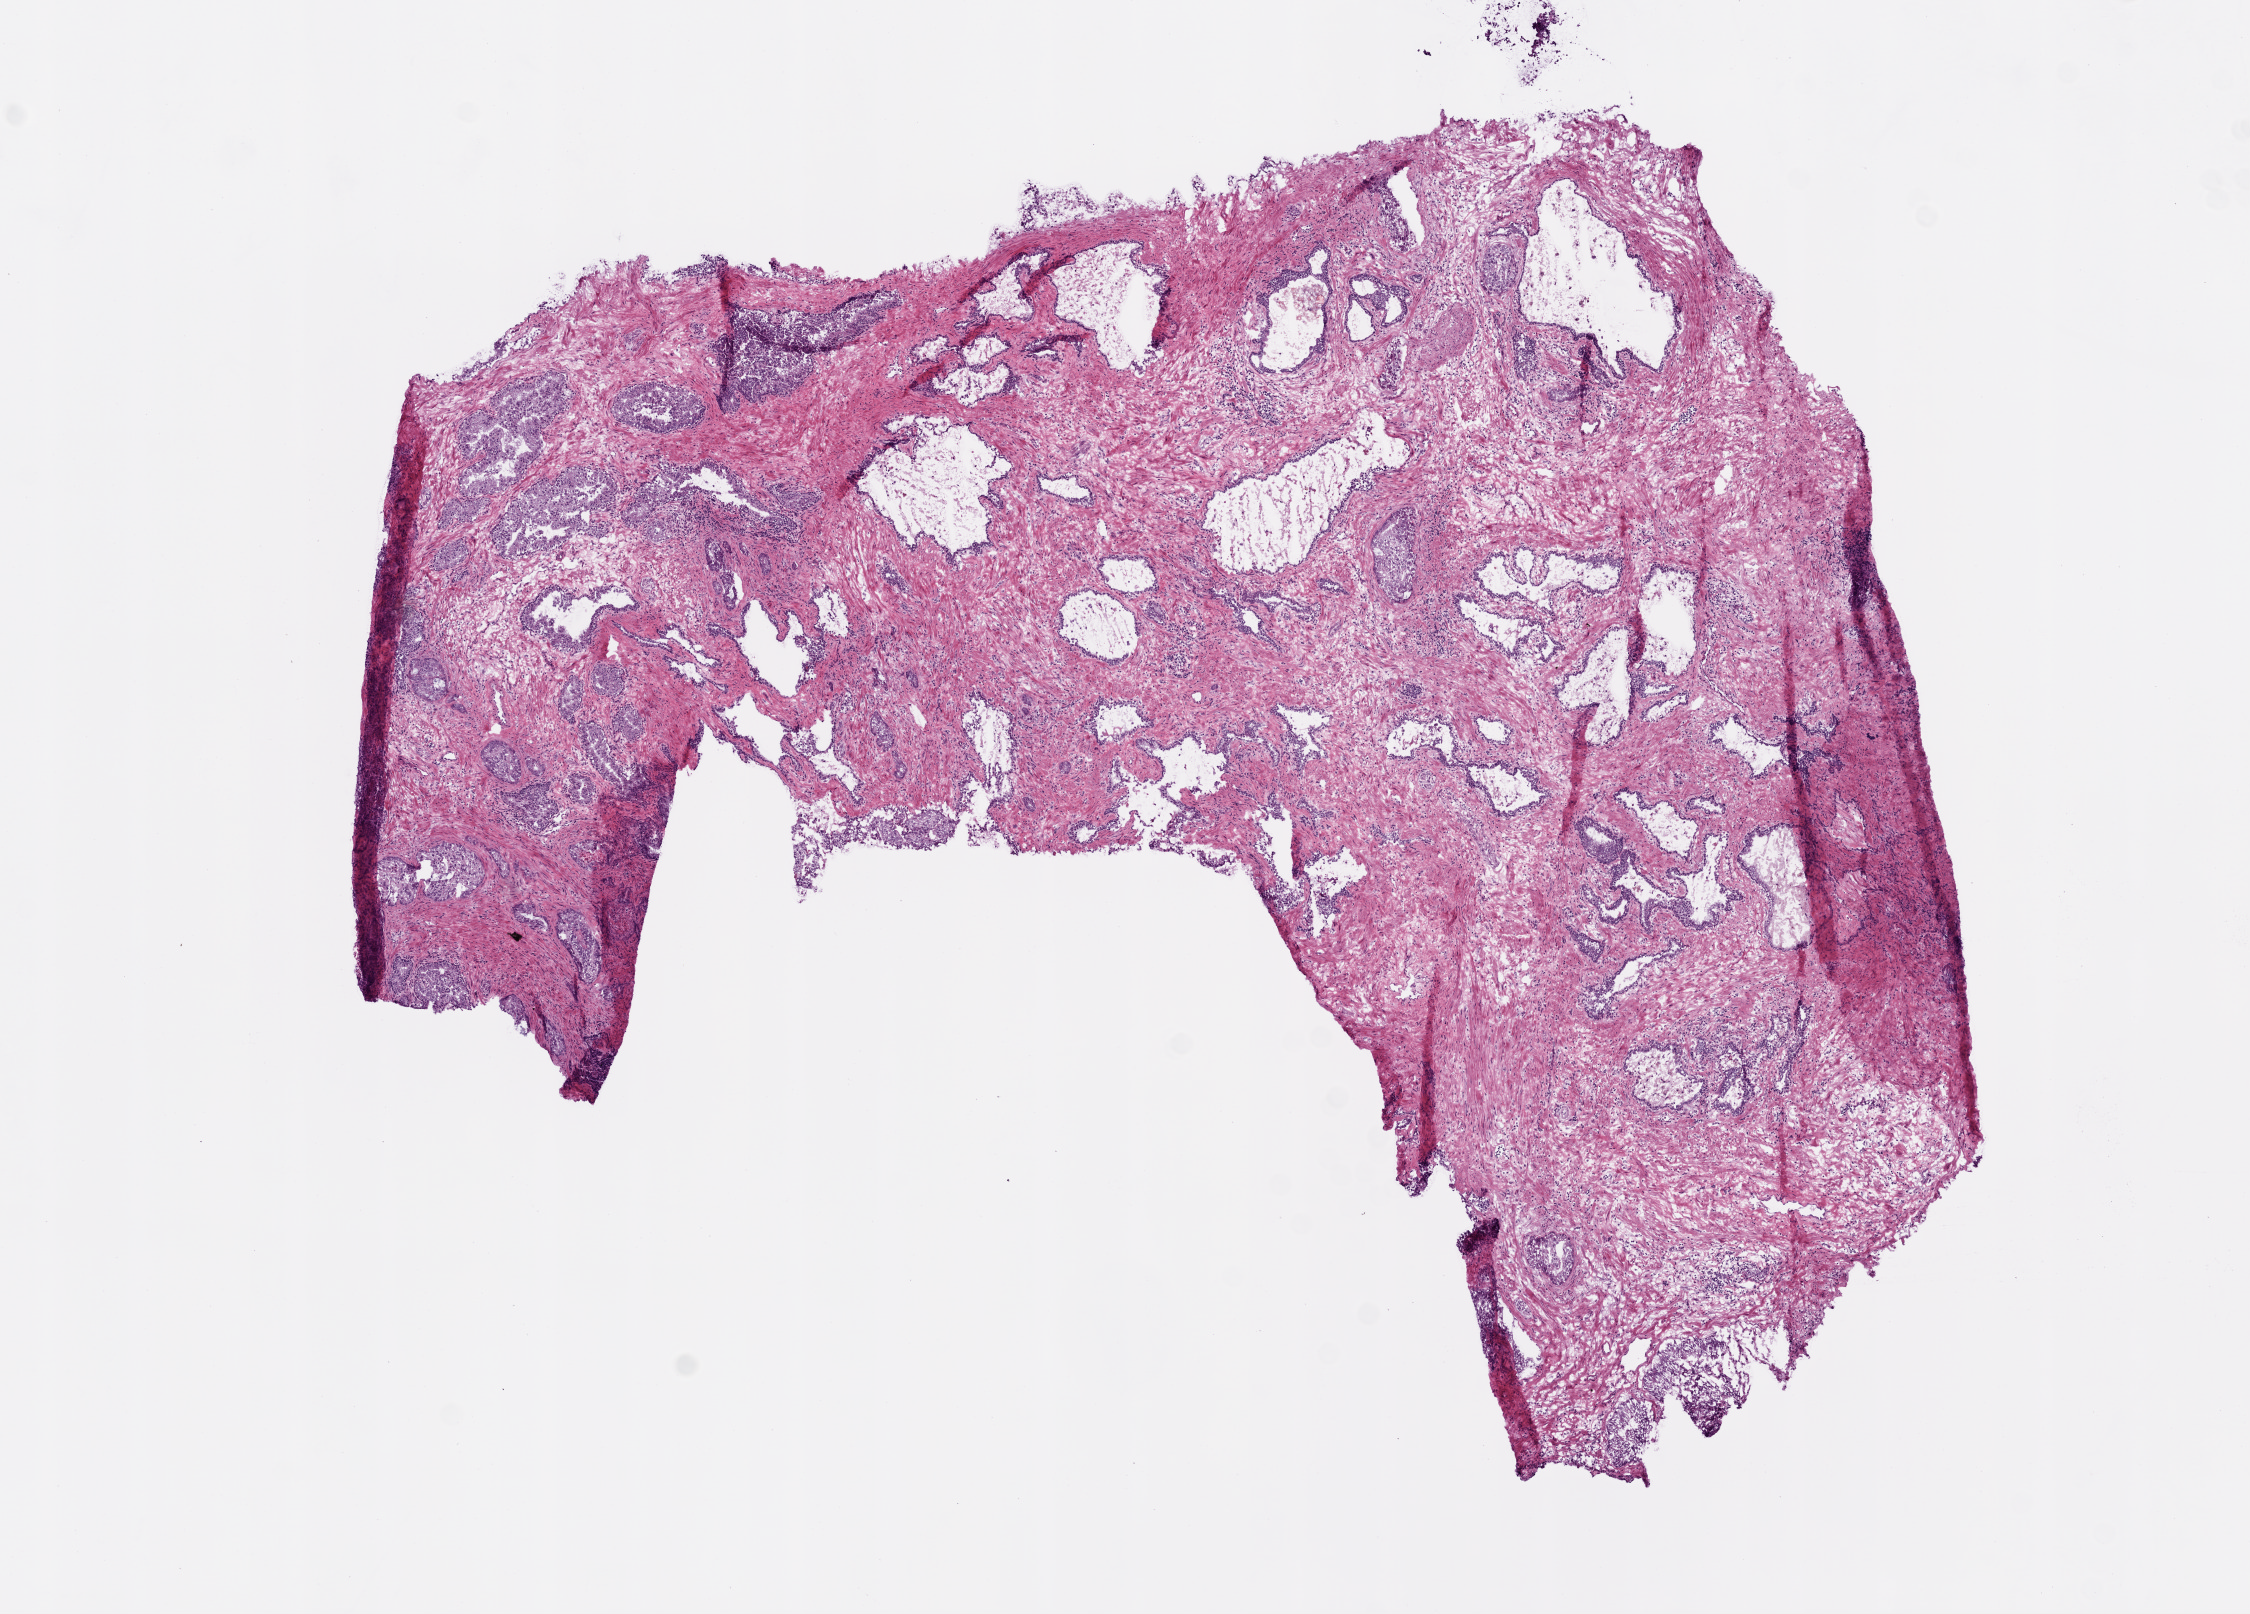
H&E whole-slide image — whole scanned area (about 9.0 x 6.5 mm) shown as a low-resolution overview. Frozen section from the top of the tissue portion. Sample: solid tissue normal (non-tumour tissue), prostate. Male, age 48 years at initial diagnosis.
* this section: solid tissue normal sample (biorepository sample class)
* patient diagnosis: Acinar cell carcinoma (prostate gland)